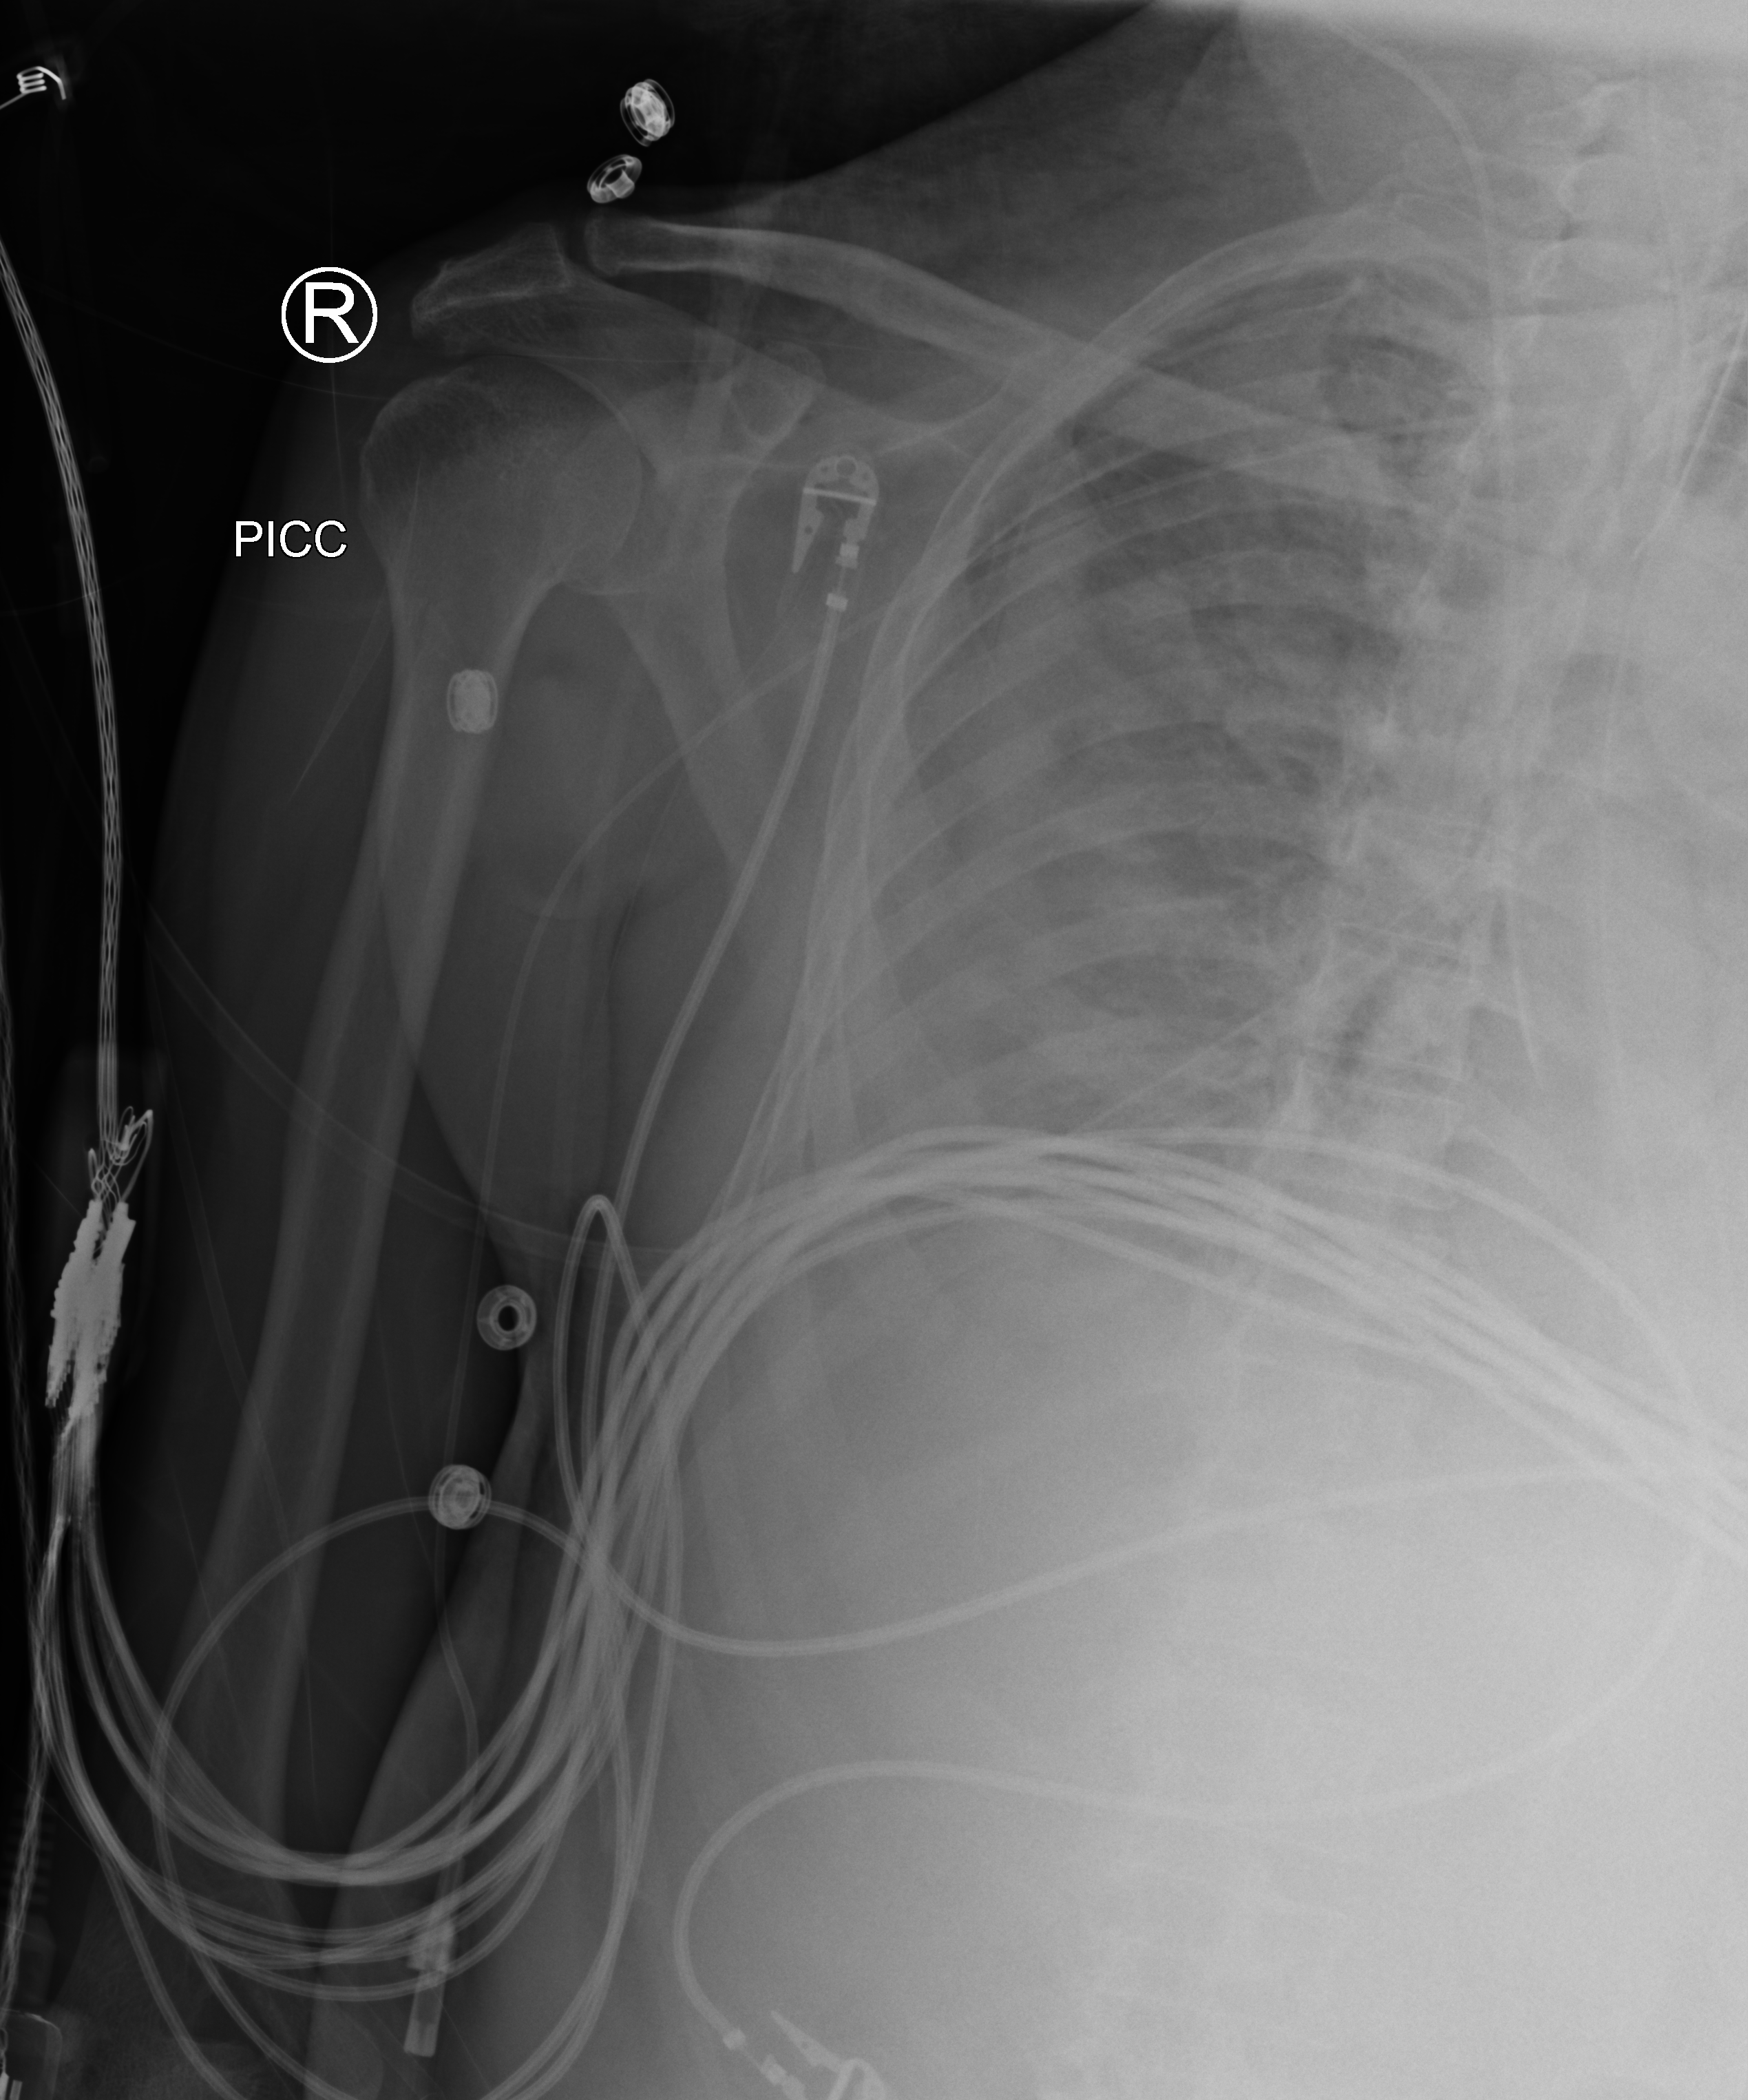
Chest X-ray (portable), anteroposterior (AP) projection. Patient hospitalised with COVID-19; male, aged 18–59 years.
From the hospital-stay record, not from the radiograph (when in the stay this image was taken is not recorded):
- admitted to intensive care during this hospital stay: yes
- mechanically ventilated during this hospital stay: yes